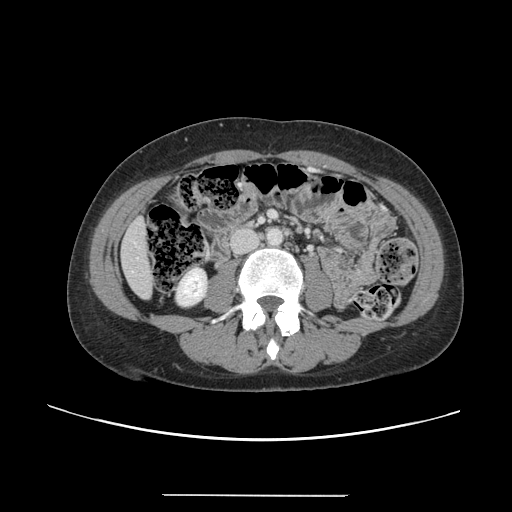
Contrast-enhanced abdominal CT, one axial slice; position 25 of 144 along the scan axis; 120 kVp; intravenous contrast given; soft-tissue window (W 400 / L 40 HU); 512 × 512 image matrix. Female patient, age 53 years. Case-level facts recorded for this patient, not image findings: diagnosis: colorectal cancer liver metastases, imaged before liver resection; multiple liver metastases: yes; largest metastasis: 1.1 cm; disease in both lobes: no.
Annotated regions visible in this slice (expert manual segmentation):
- liver: bounding box (x1, y1, x2, y2) in pixels: (122, 215, 153, 298)
- planned liver remnant (the part of the liver to remain after resection): (121, 215, 153, 298)